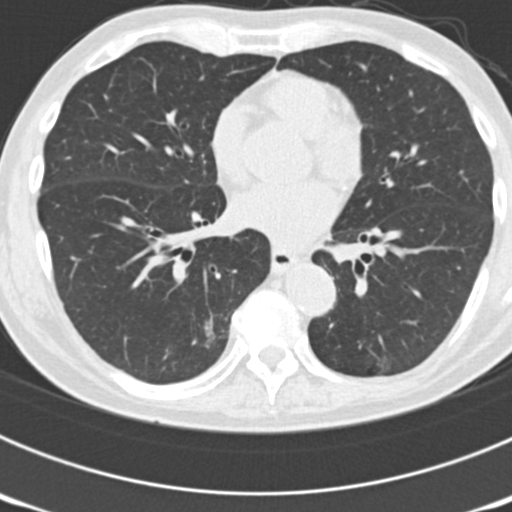
Axial slice from a low-dose chest CT screening exam. Third screening round (two years after baseline). Lung window (W 1500 / L -600 HU). Standard (soft-tissue) reconstruction kernel (B30f). Slice 90 of 177 in the series. Male, age 70 years at enrolment. Current smoker at enrolment.
- Expert reader's lesion annotation, bounding box [x1, y1, x2, y2] px = [150, 298, 240, 384].
- The screening reader recorded 3 non-calcified nodules or masses ≥4 mm on this exam; which of them this box marks is not recorded.
- Official screen result: positive, other.
- Lung cancer was diagnosed 14 days after this screen: bronchiolo-alveolar adenocarcinoma, NOS, right lower lobe, poorly differentiated (G3), stage IB (AJCC 6th edition), 30 mm at pathology.